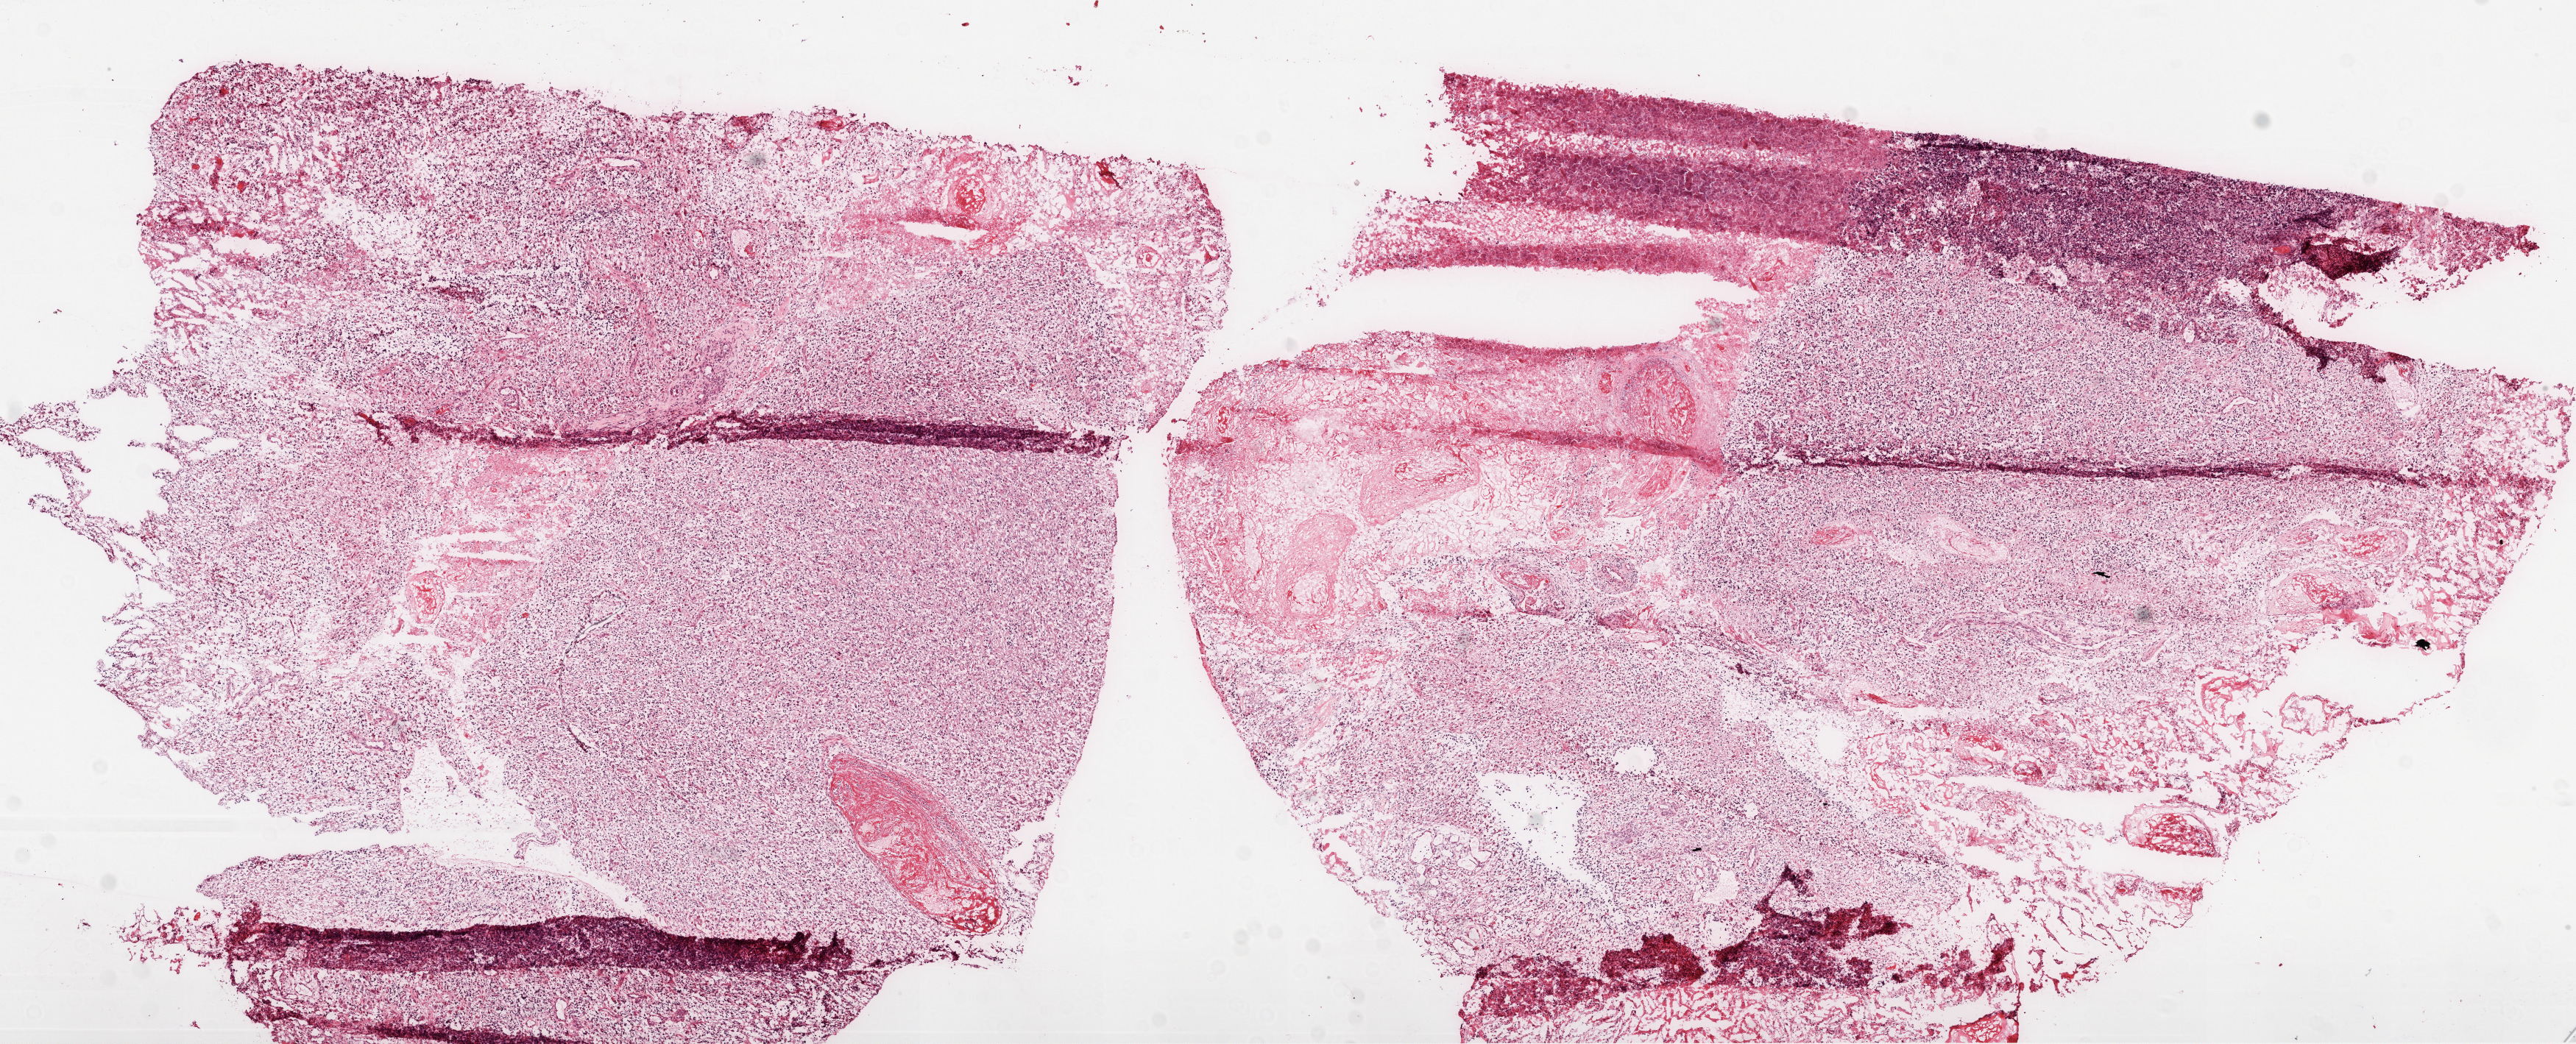
Whole-slide histology image, H&E-stained — a low-resolution overview of the entire scanned area, about 14.0 x 5.7 mm (slide scanned at 20x), frozen section, primary tumour sample from the brain. Male, age 39 years at initial diagnosis. Pathologist review of this section (percent, as recorded): tumour cells 75%, tumour nuclei 100%, normal cells 0%, stromal cells 0%, necrosis 25%.
Pathologic diagnosis: Glioblastoma.